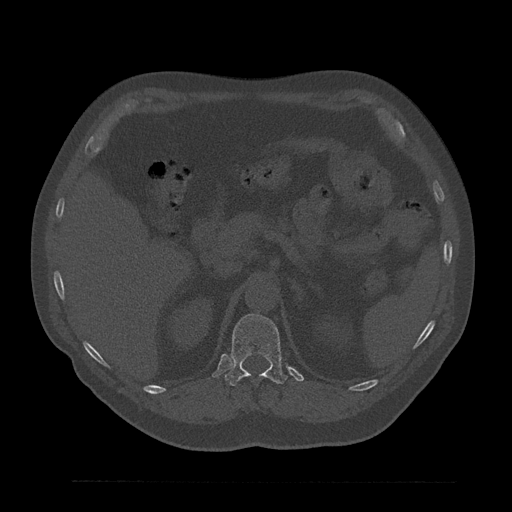
CT including the spine, one axial slice. Slice 236 of 797 in the series (ordered by position). Reconstruction kernel Br40s/3. 120 kVp. Bone window (W 1800 / L 400 HU). 0.5 mm slice thickness. 512 × 512 image matrix. Patient: male, 61 years. From the clinical record (not read from this slice): primary cancer: prostate.
Annotated regions visible in this slice (semi-automatically segmented with operator editing):
- T12 vertebra: bounding box (x1, y1, x2, y2) in pixels: (225, 314, 287, 387)